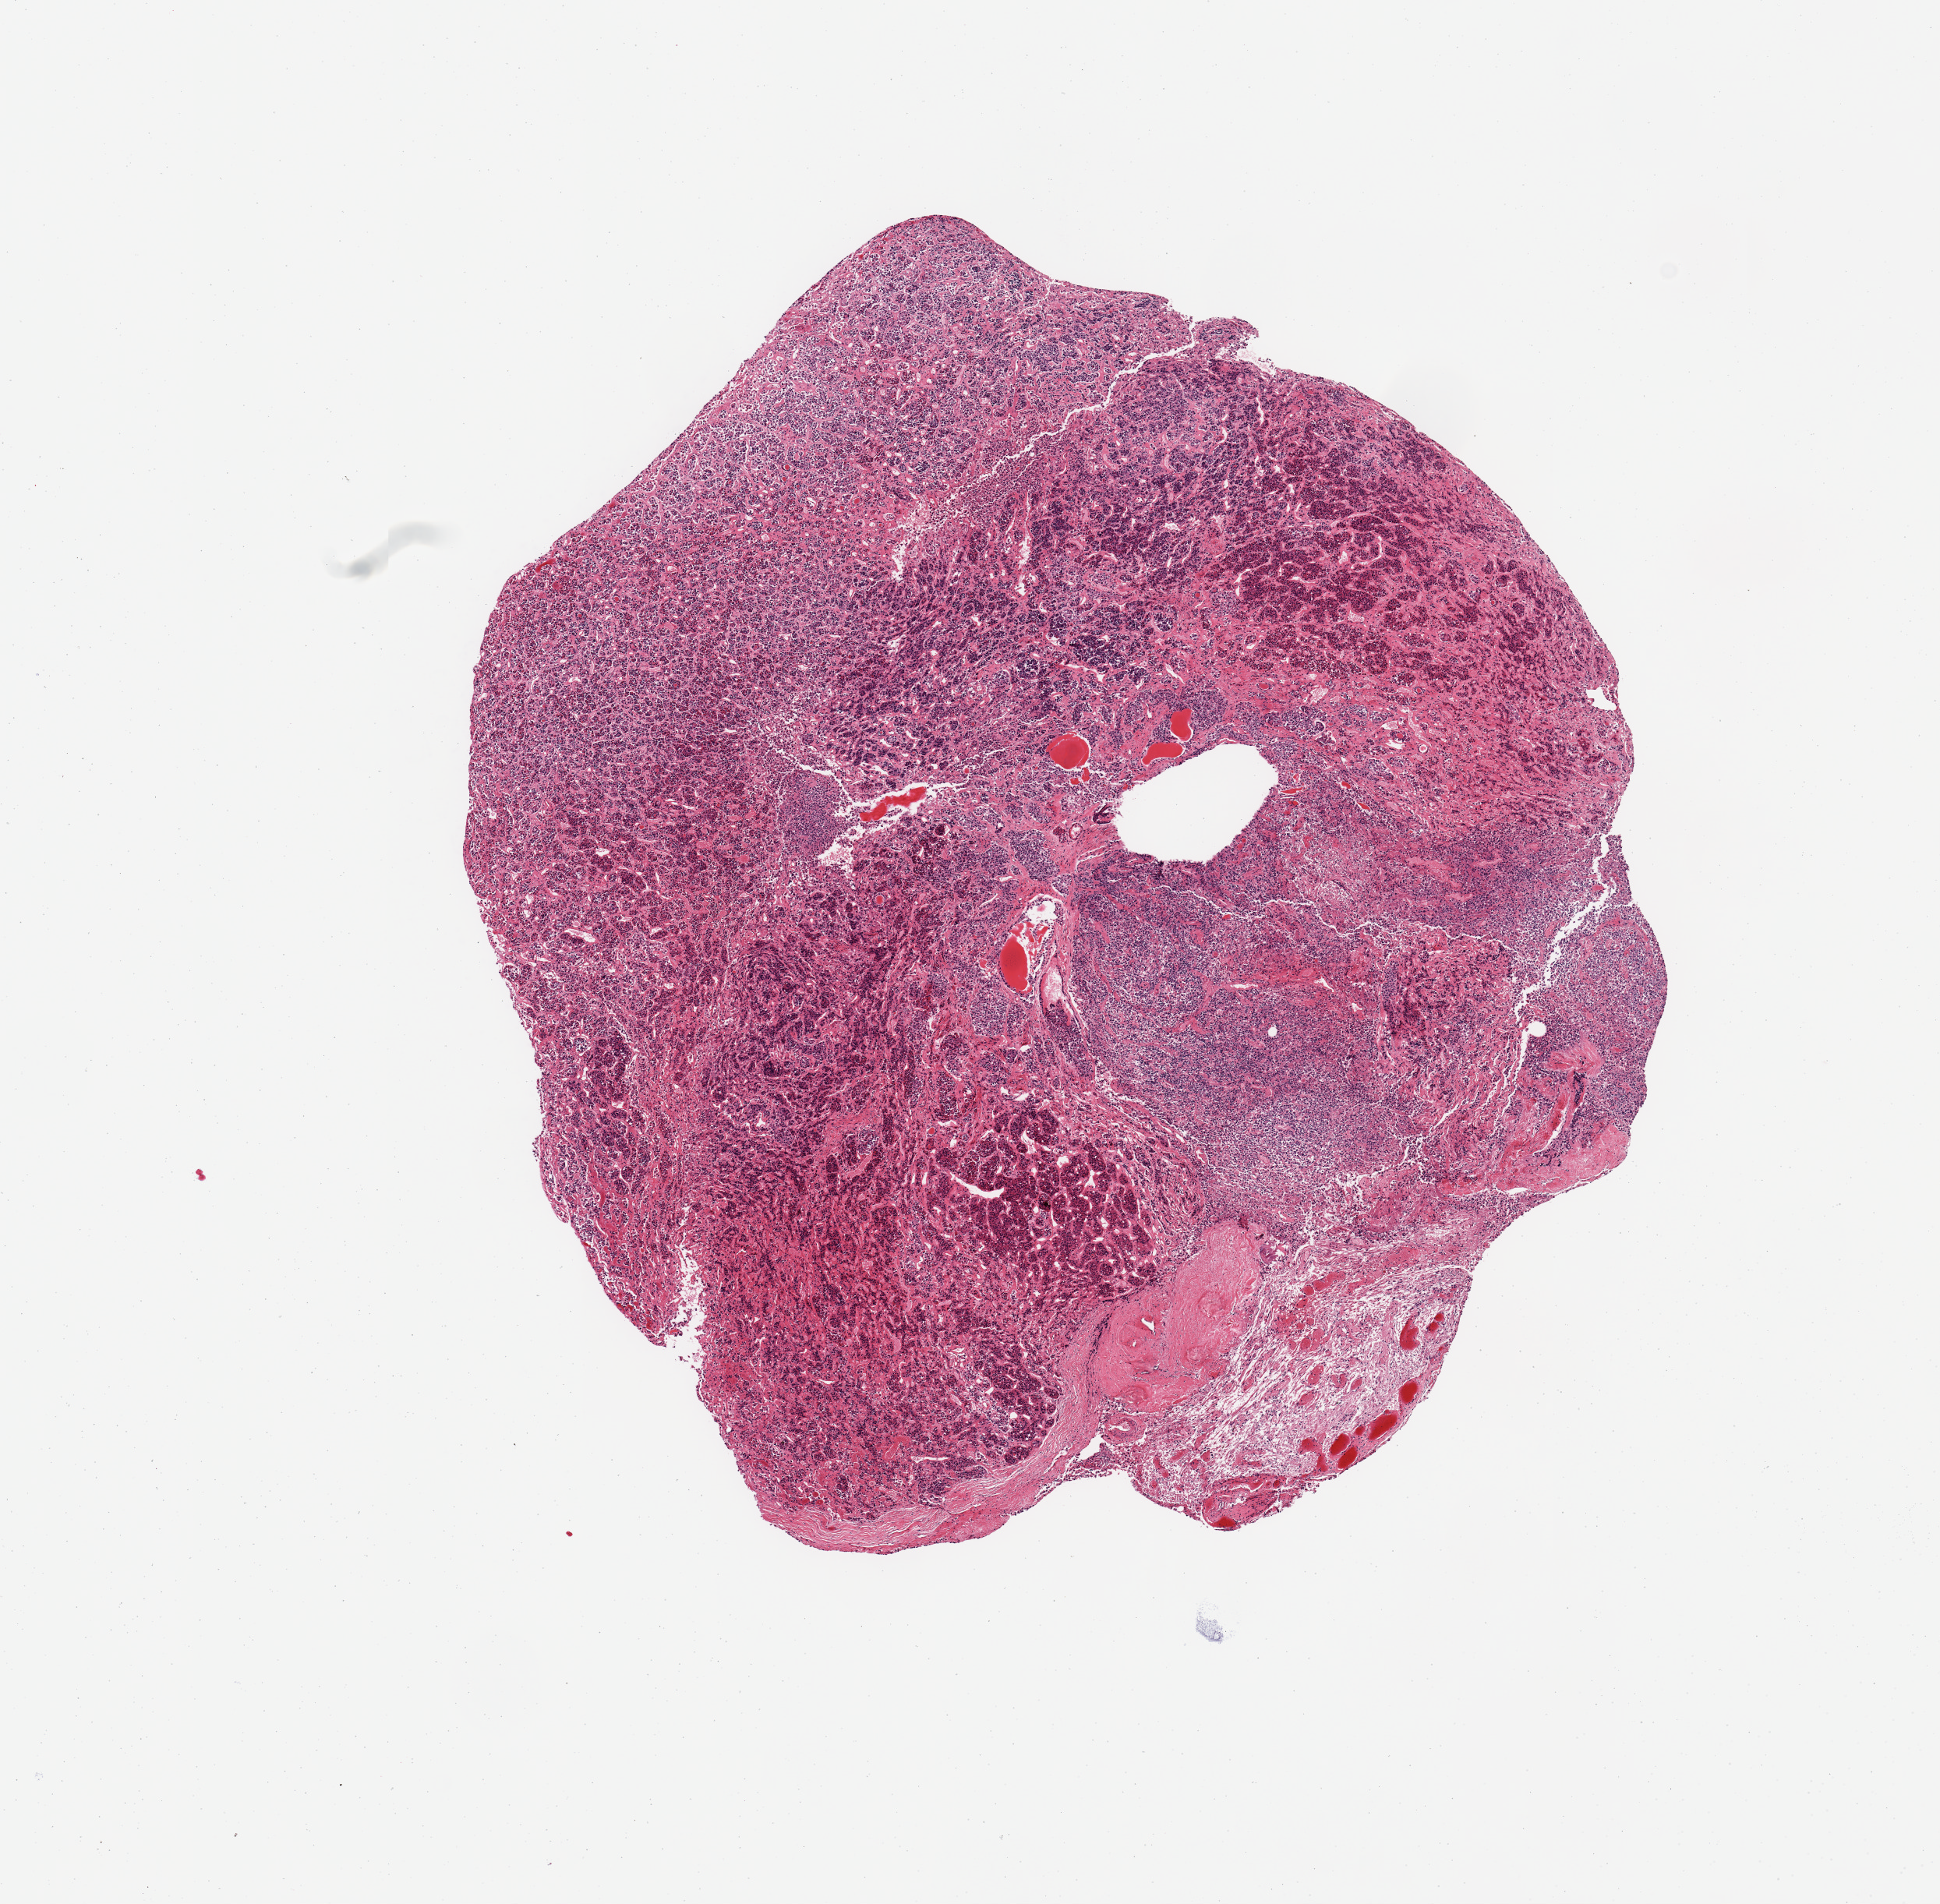
Whole-slide image, H&E stain — shown as a low-resolution overview of the whole scanned area (about 9.8 x 9.7 mm); PAXgene-fixed, paraffin-embedded tissue; target tissue: pituitary; tissue donor sample. Donor sex: male.
* pathologist's review note for this sample: 1 piece; mostly anterior lobe